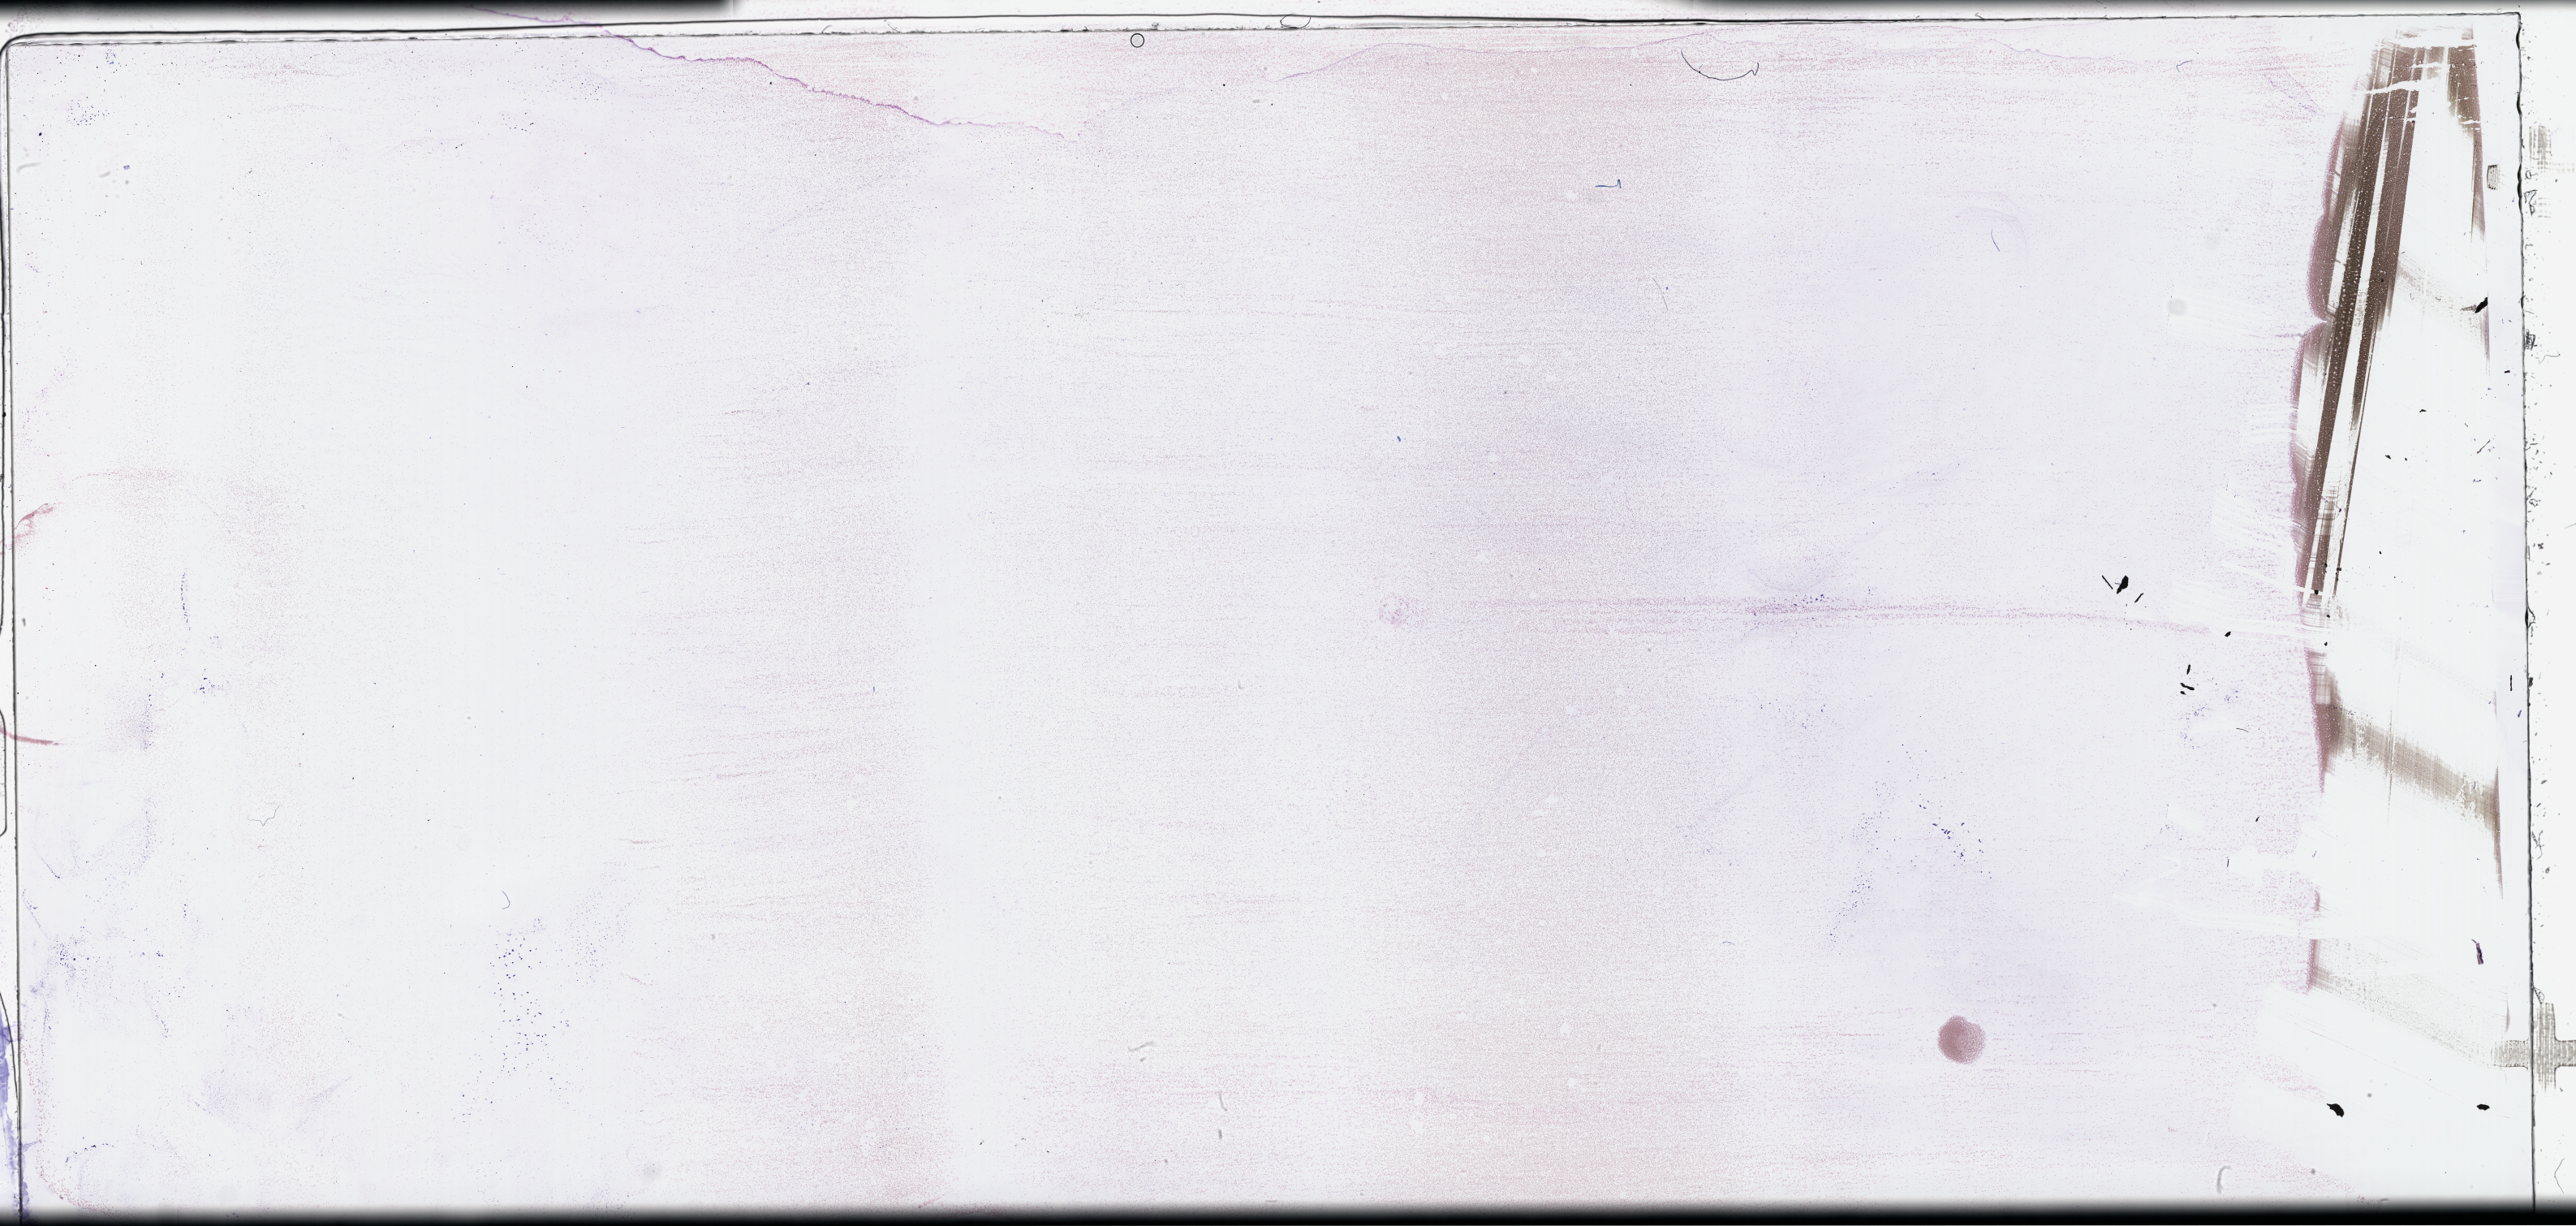
Whole-slide image of a whole blood smear, Wright–Giemsa stain, low-resolution overview of the scanned area, about 51.3 x 24.4 mm; smear from an EDTA sample; collected at disease progression. Patient sex: male.
From a patient with: Plasma Cell Myeloma.